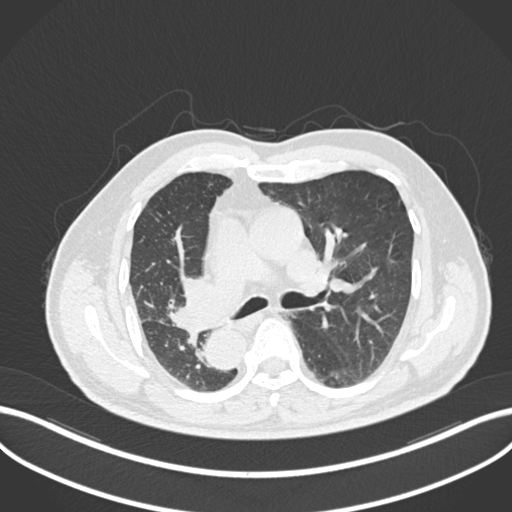
Chest CT, one axial slice. Slice 137 of 206 in the series (ordered by position). Reconstruction kernel B30f. 120 kVp. Lung window (W 1500 / L -600 HU). 1 mm slice thickness. 512 × 512 image matrix. Patient: male, 67 years. From the clinical record (not read from this slice): clinical TNM (as recorded): T2a N0 M0.
Outlined on this slice (bounding box drawn by a radiologist):
- lung tumour (recorded histology: squamous cell carcinoma): box from (x=164, y=271) to (x=231, y=336) px